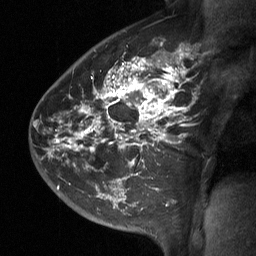
Breast MRI (dynamic contrast-enhanced), one sagittal slice; position 44 of 64 along the scan axis; dynamic contrast-enhanced study with each time point stored as its own series, time point 2 of 3 at this slice position (early post-contrast, ordered by acquisition time); 1.5 T; TE 4.8 ms, TR 27 ms; 2 mm slice thickness; 256 × 256 image matrix. Female patient, age 42 years. Case-level facts recorded for this patient, not image findings: setting: breast cancer imaged before/during neoadjuvant chemotherapy; receptor status: triple-negative.
Structures marked on this image (semi-automatic segmentation, software-assisted and operator-edited):
- analysis volume of interest (the breast-tissue region the enhancement analysis was run in; not a lesion): bounding box (x1, y1, x2, y2) in pixels: (49, 45, 197, 197)
- tumour enhancement mask (voxels above the 90 % enhancement threshold inside the analysis volume of interest): (49, 48, 188, 175)